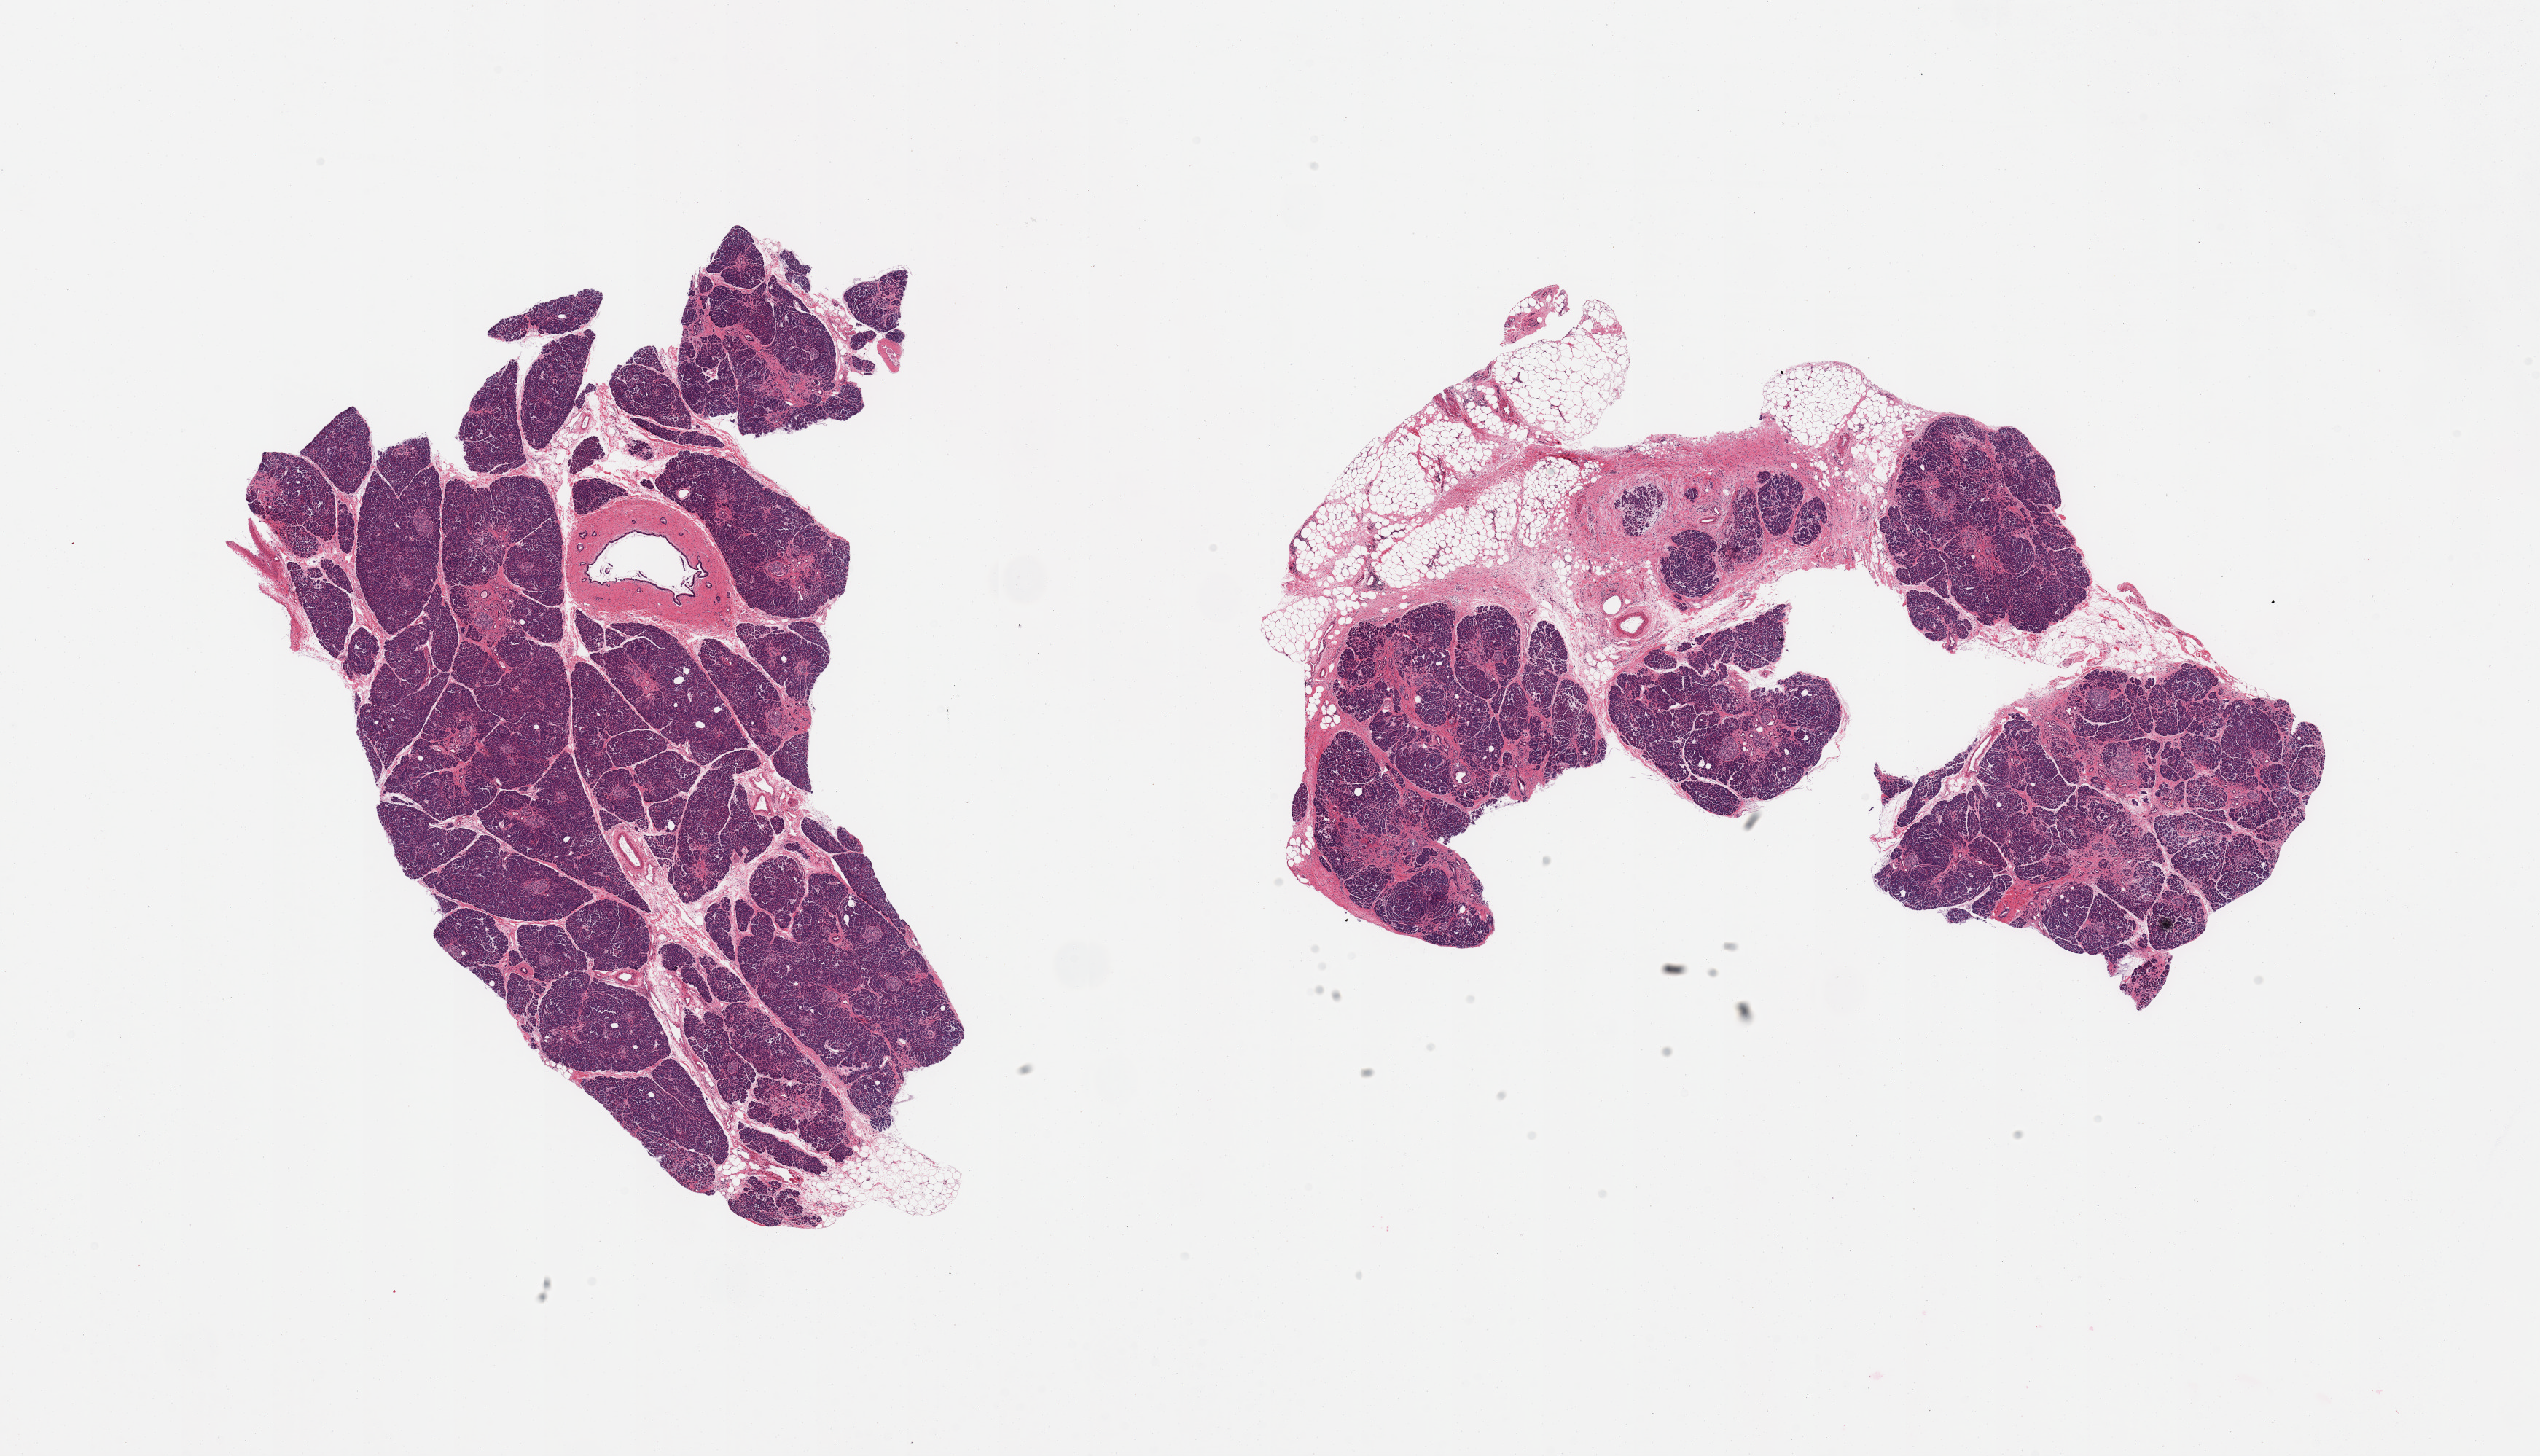
Digitized hematoxylin and eosin (H&E)-stained section — a low-resolution overview of the entire scanned area, about 27.6 x 15.8 mm (acquisition: 20x scan). PAXgene-fixed, paraffin-embedded tissue. Target tissue: pancreas. Tissue donor sample.
Review note (as recorded): 2 pieces; multiple foci of fibrosis (probable healed pancreatitis); 30% external fat on 1, 20% on other.